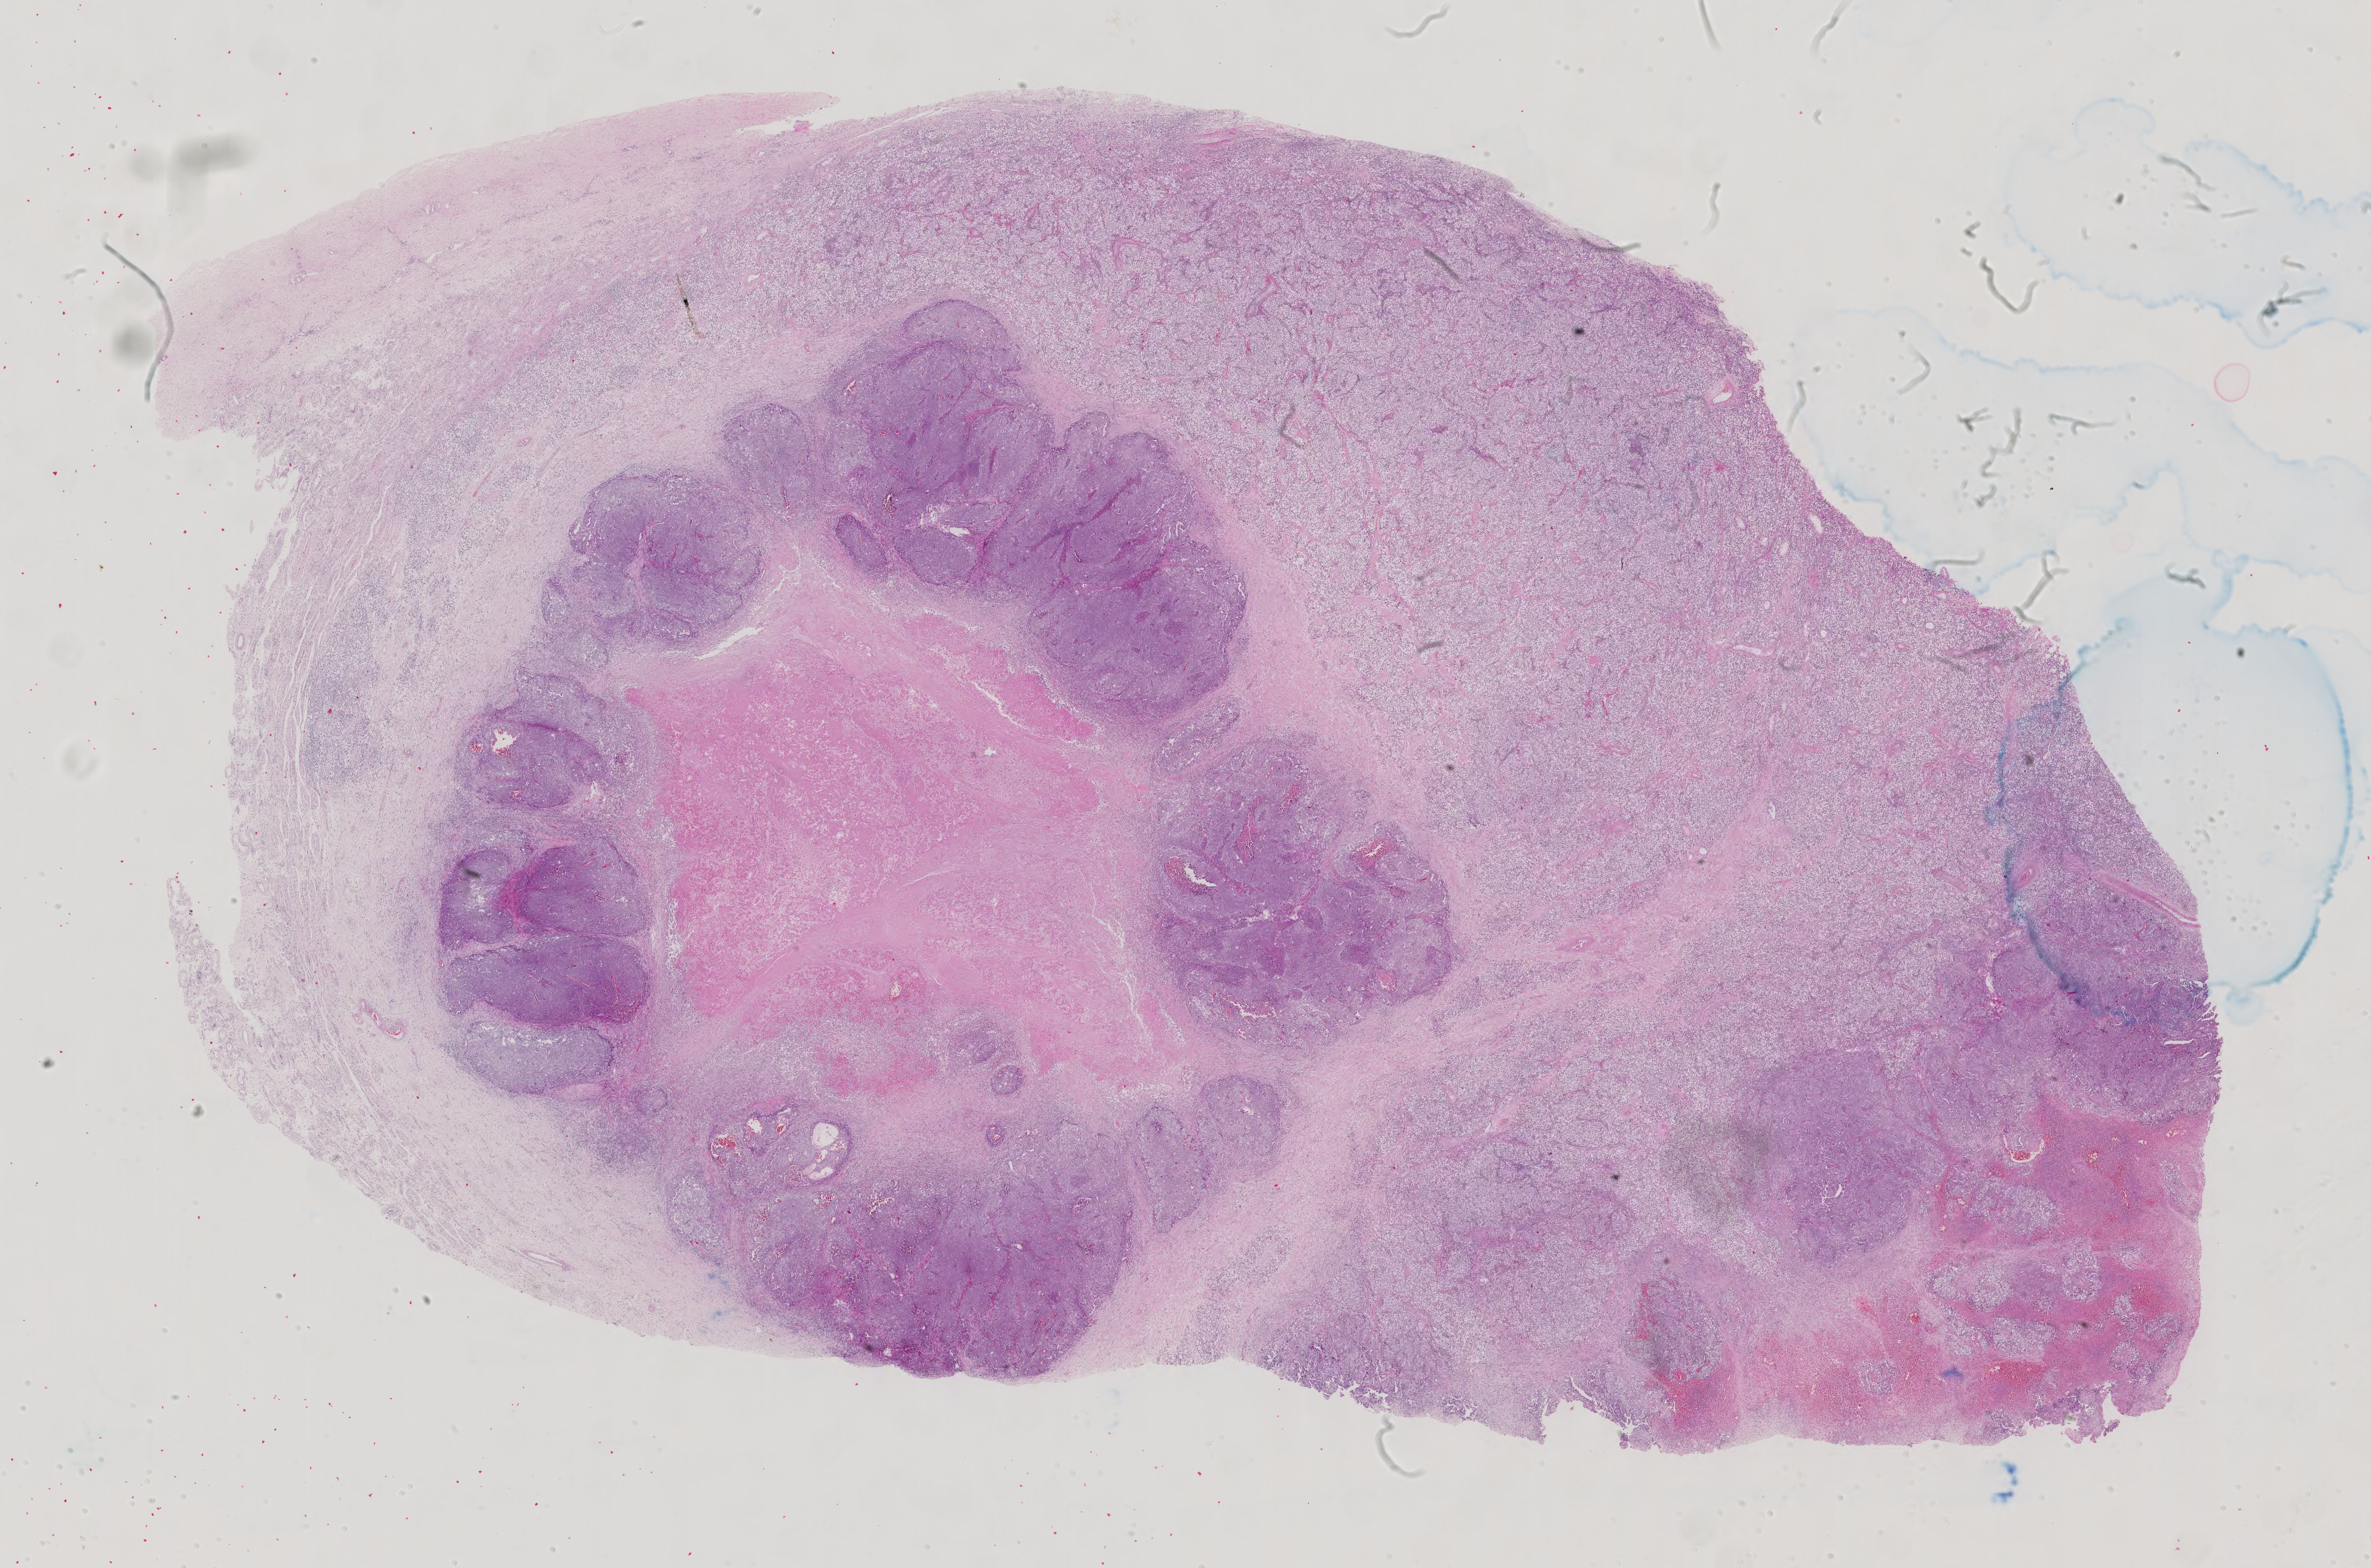
Digitized Hematoxylin and eosin (H&E) stained tissue section (whole slide), whole scanned area (about 28.9 x 19.1 mm) shown as a low-resolution overview; FFPE section; sample: primary tumour, testis. Male, age 28 years at initial diagnosis.
* AJCC pathologic stage: IA (6th edition)
* pathologic diagnosis: Mixed germ cell tumor